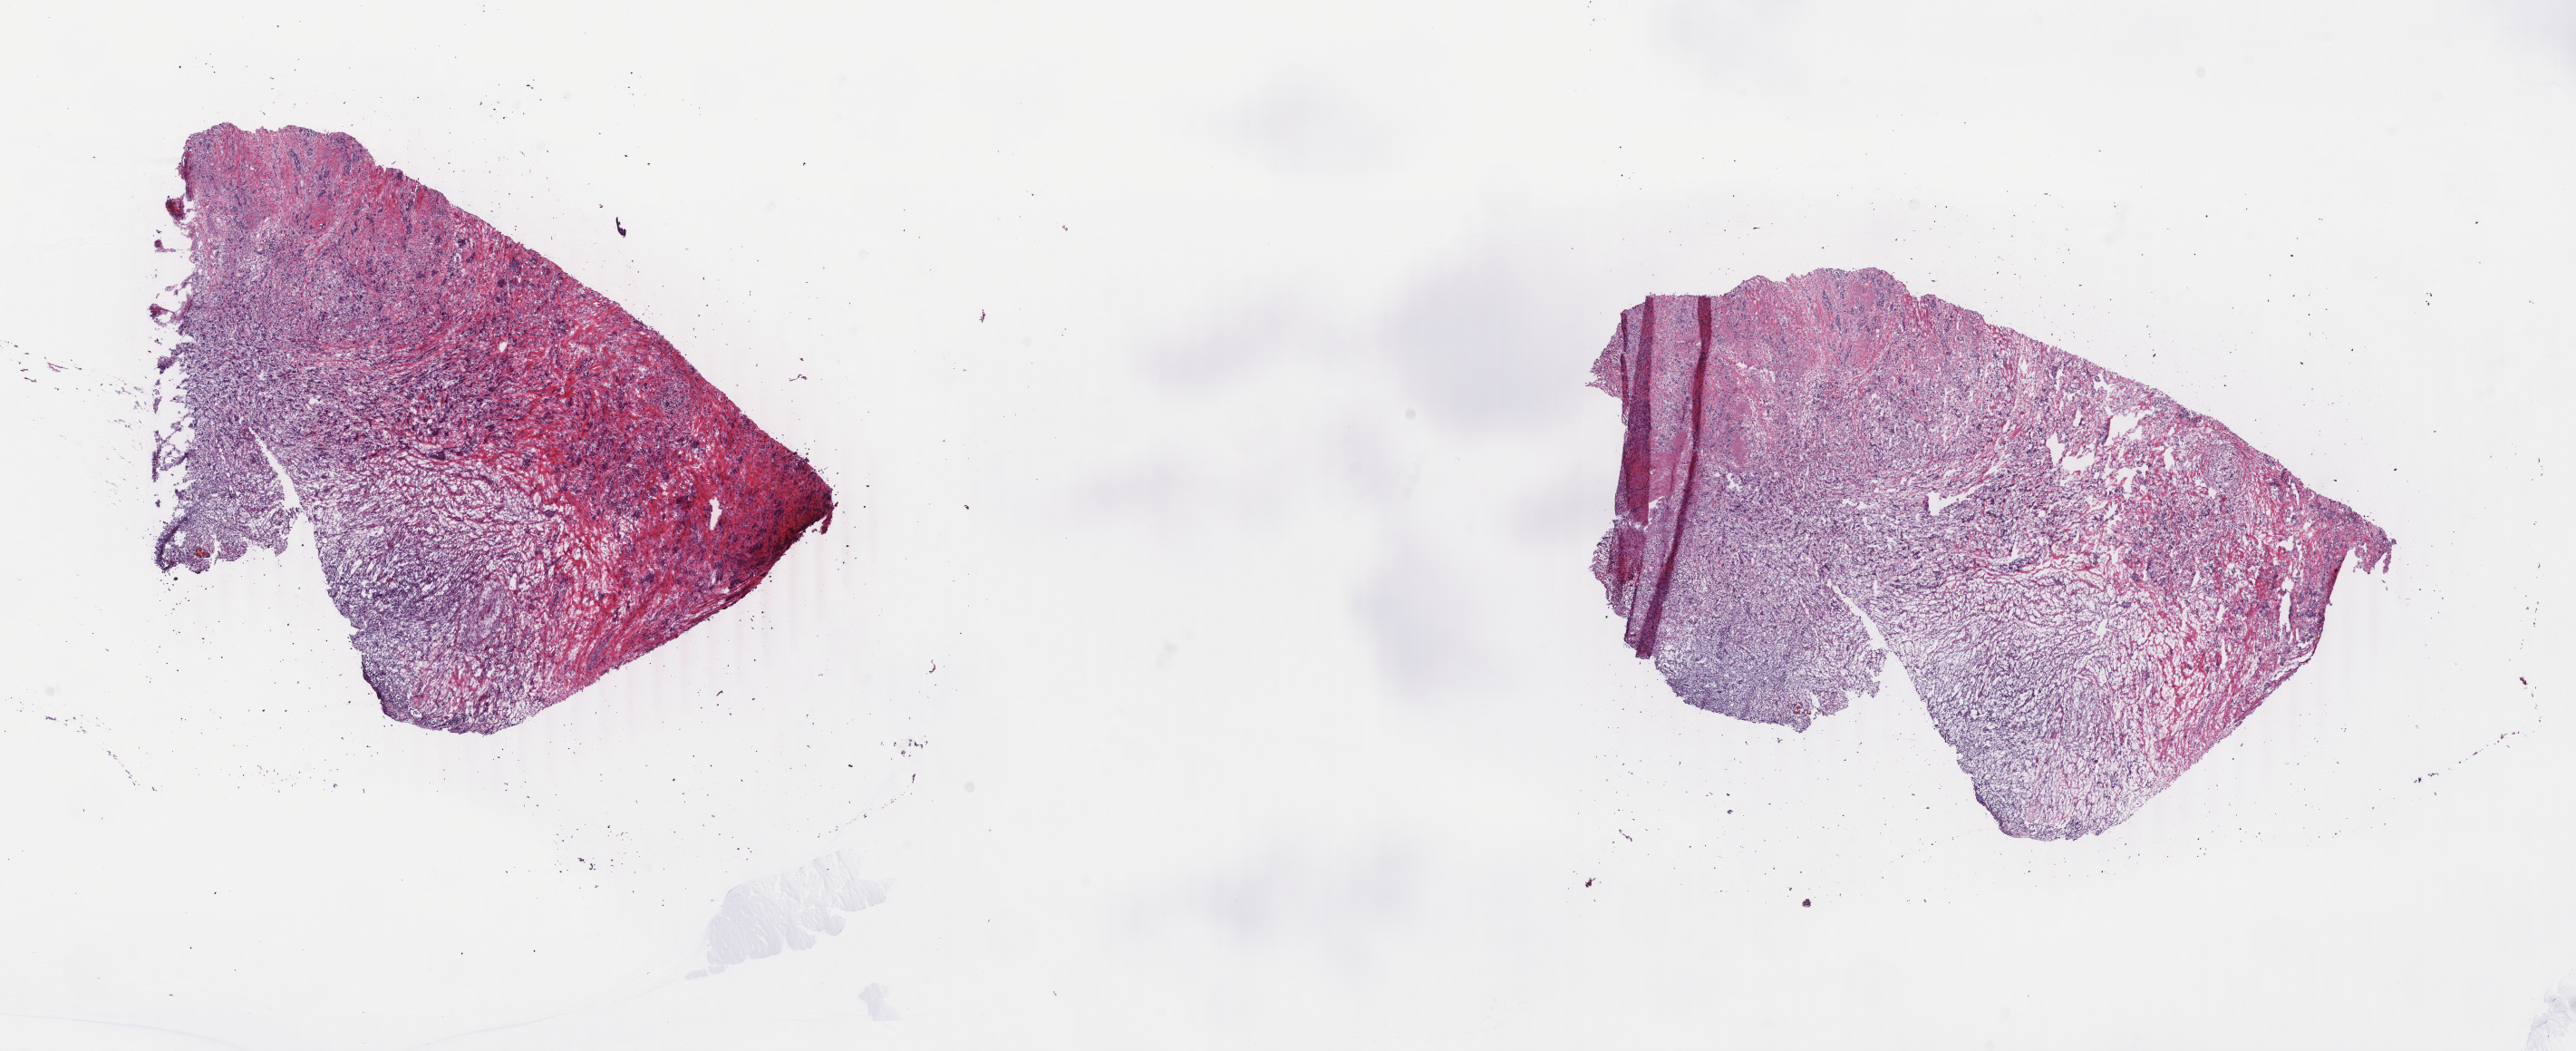
H&E-stained whole-slide image, whole scanned area (about 22.6 x 9.2 mm) shown as a low-resolution overview. Frozen section from the top of the tissue portion. Primary tumour sample from the bladder. Female patient; age at initial diagnosis 84 years. Histologic grade: high grade. Pathologist review of this section (percent, as recorded): tumour cells 70%, tumour nuclei 70%, normal cells 0%, stromal cells 30%, necrosis 0%. Infiltration values recorded for this section: lymphocyte infiltration 6%, monocyte infiltration 2%, neutrophil infiltration 1%.
Pathologic diagnosis: Transitional cell carcinoma. AJCC pathologic stage: IV (6th edition).